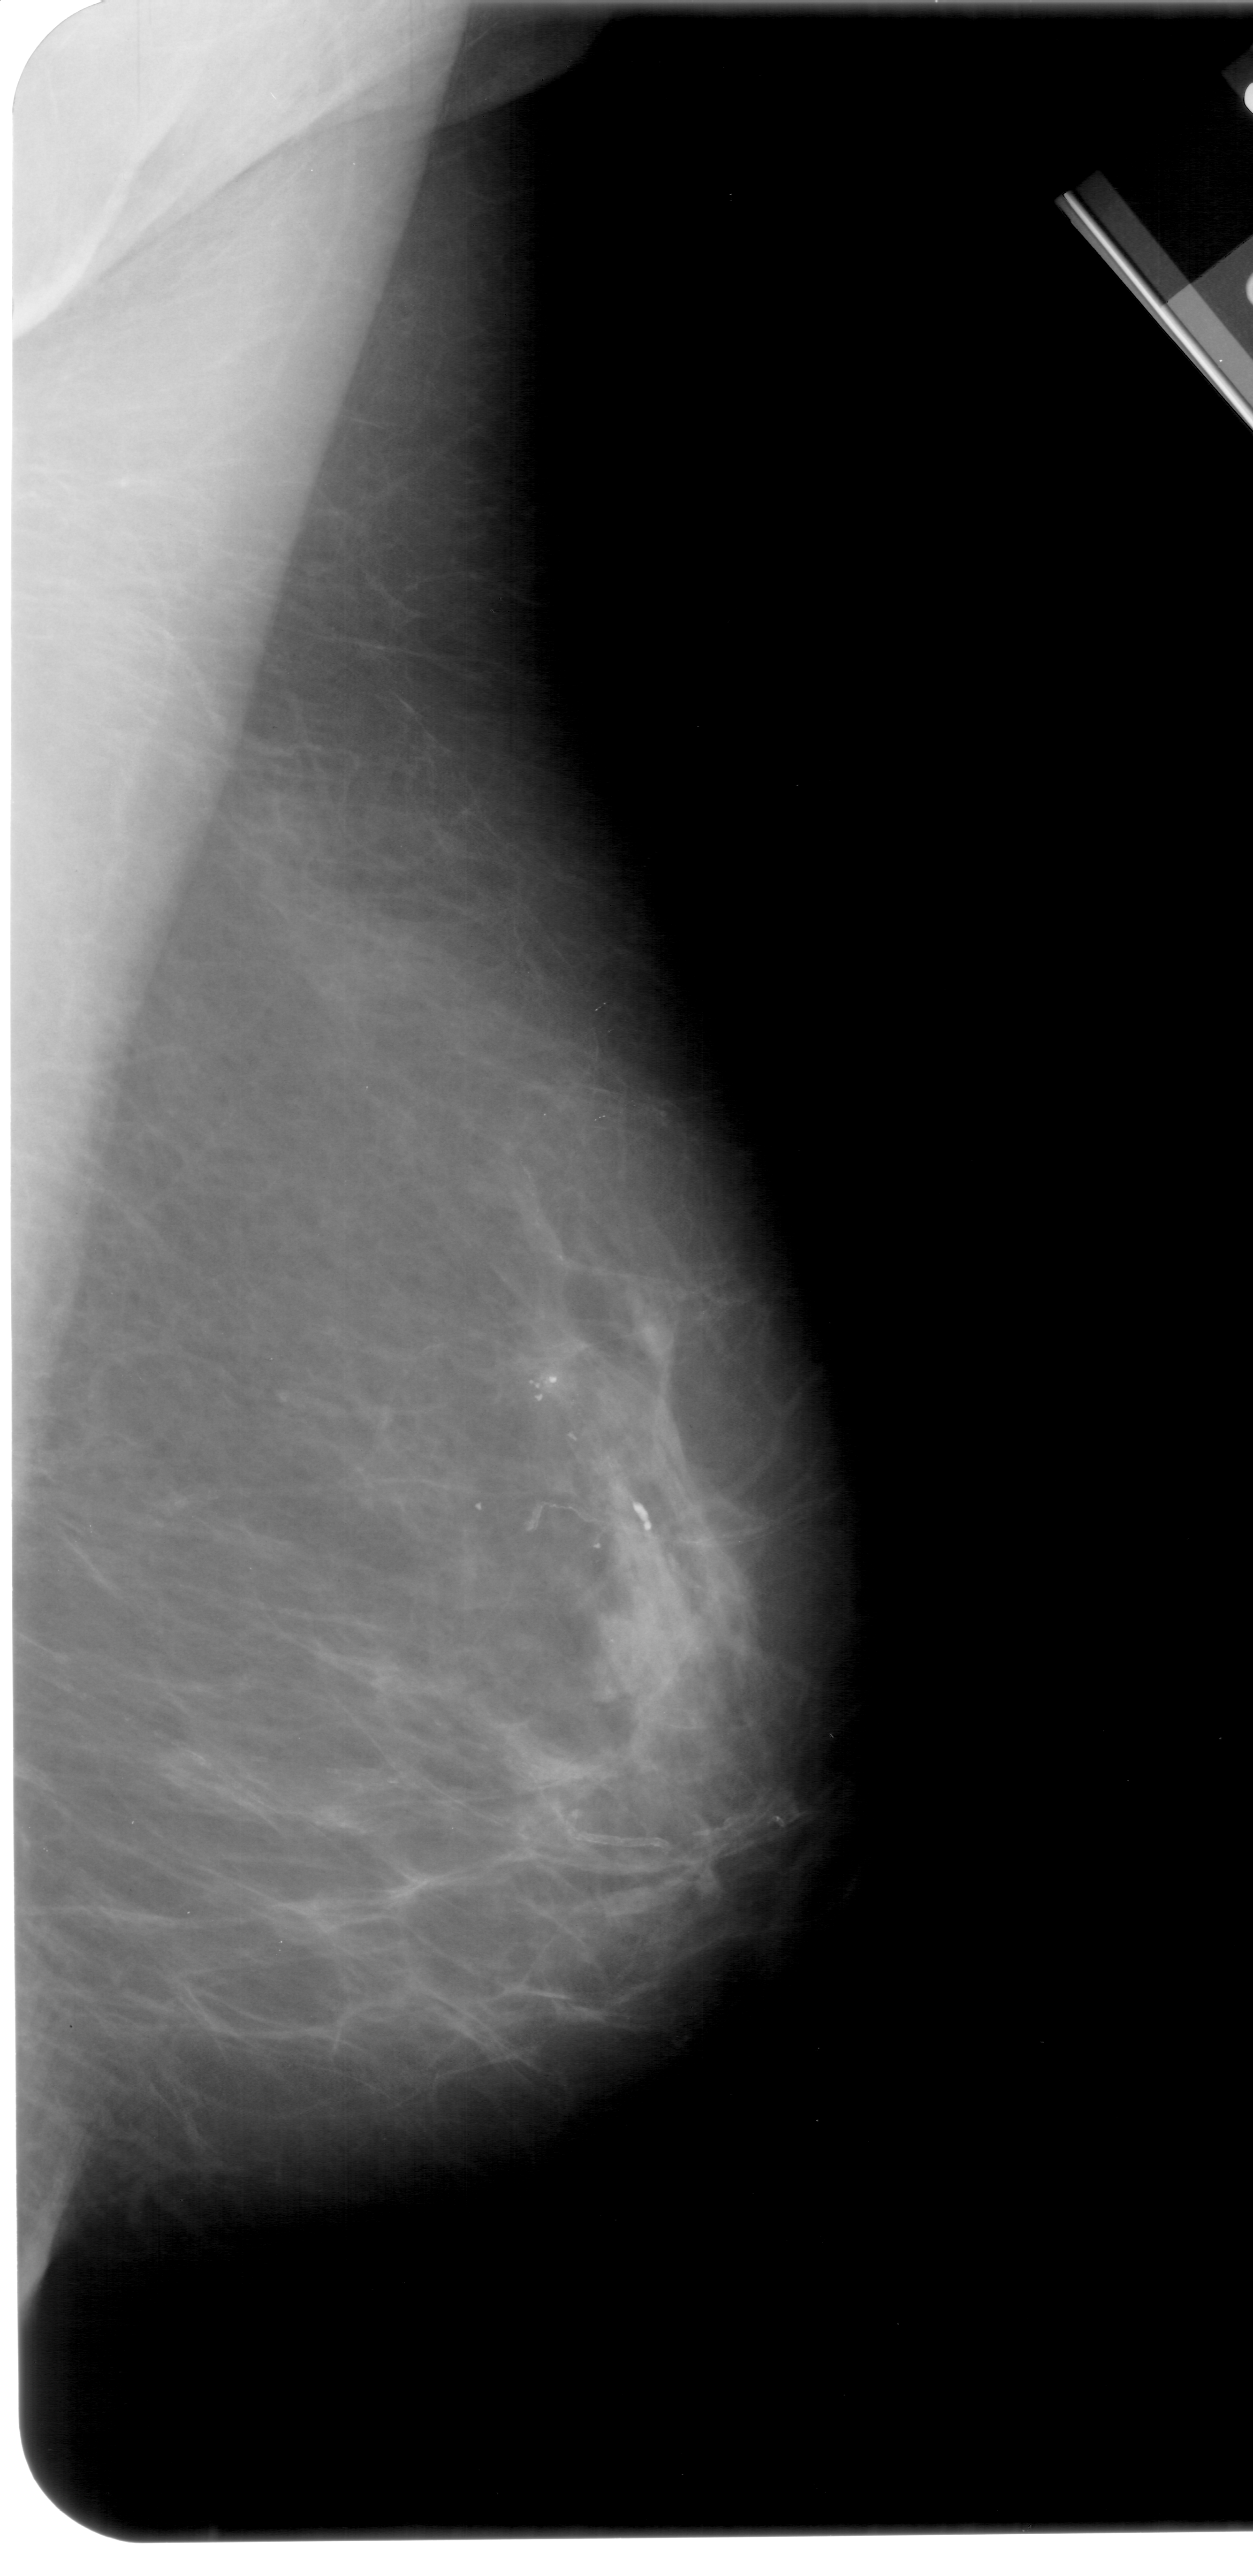
Scanned film-screen mammogram; right breast; MLO view; 1253 × 2576 image matrix.
Expert-marked regions of interest on this film, with their recorded descriptors:
- calcifications, morphology pleomorphic, distribution linear; BI-RADS assessment category 4; subtlety rating 2 on a 1 (subtle) to 5 (obvious) scale; pathology (as recorded): malignant: bounding box <474,1191,708,1587> (left, top, right, bottom; pixels)